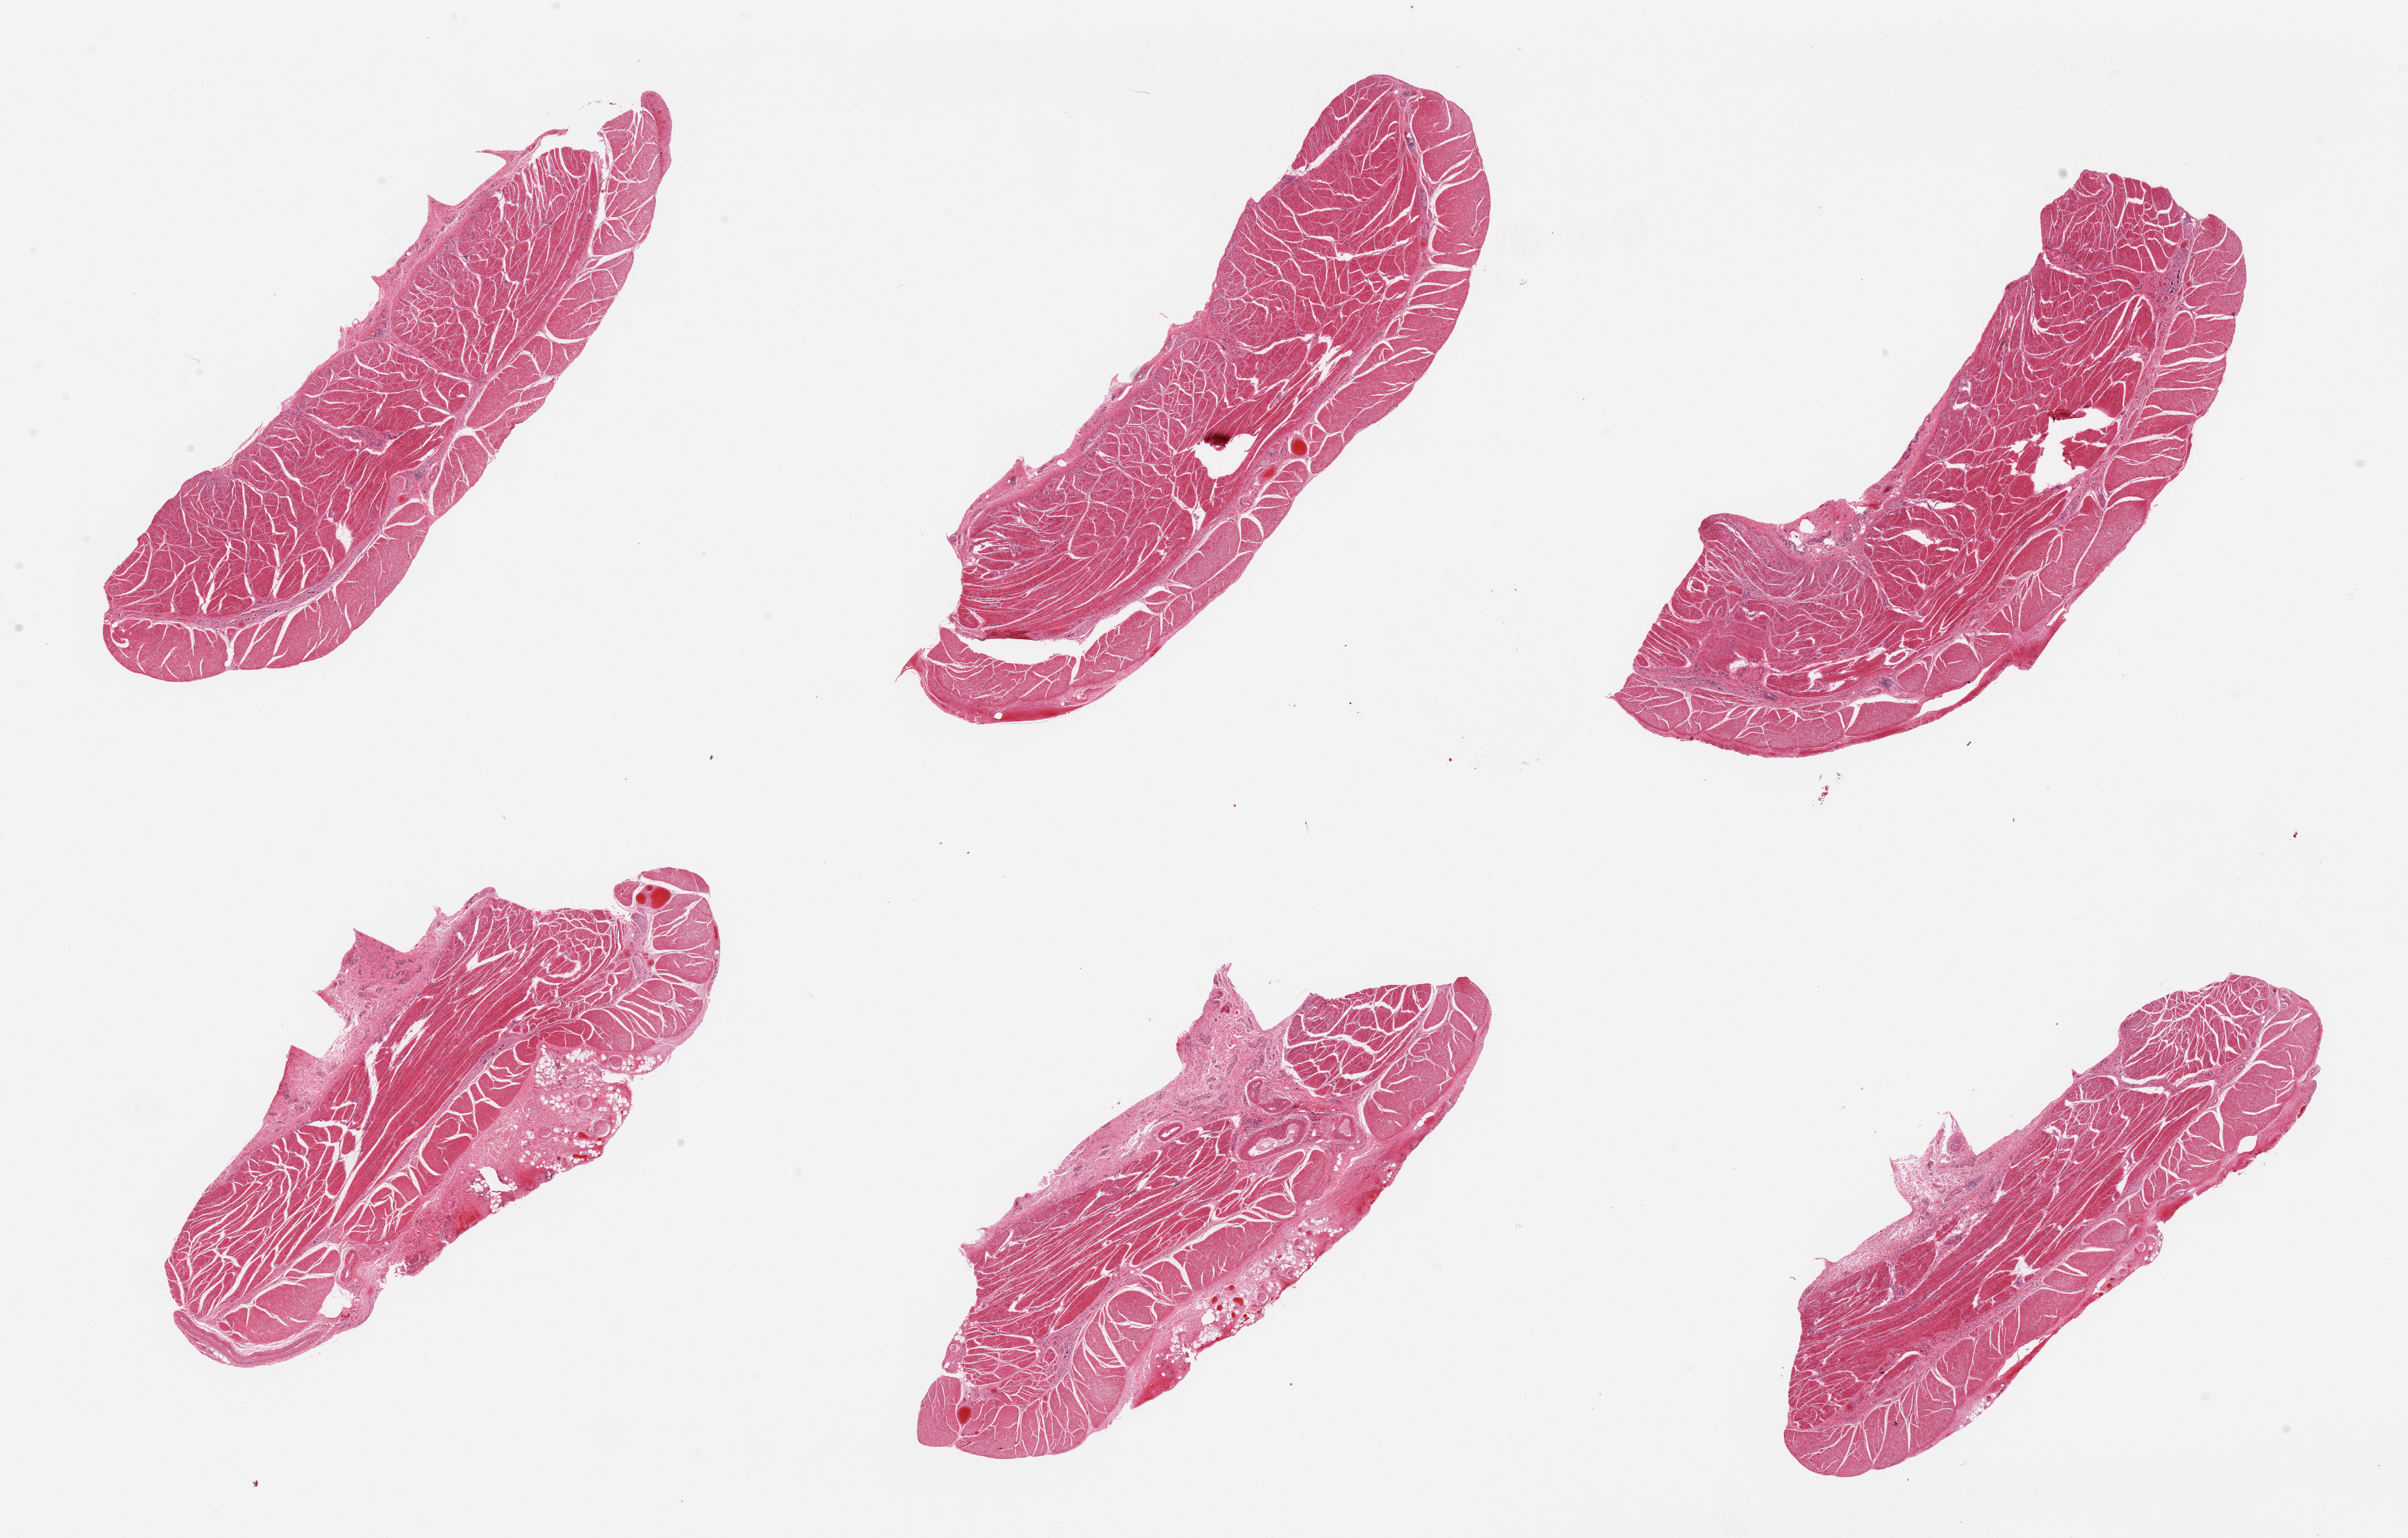
Whole-slide image, haematoxylin and eosin stain, low-resolution overview of the scanned area, about 31.5 x 20.1 mm; PAXgene-fixed, paraffin-embedded tissue; sampled site (target tissue): esophageal muscle; tissue donor sample. Donor sex: male.
Pathologist's review note for this sample: 6 pieces, all muscularis, good specimens.